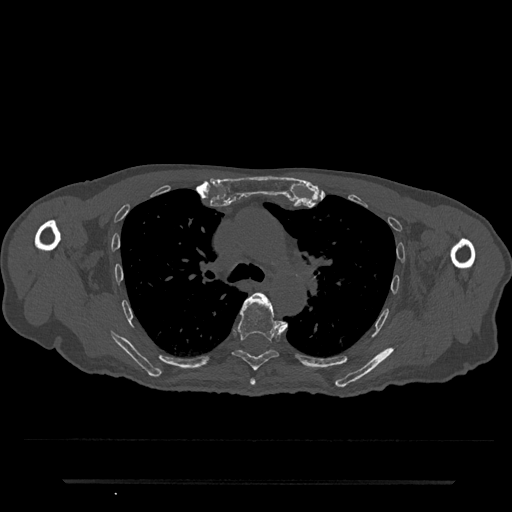
CT including the spine, one axial slice. Slice 534 of 797 in the series (ordered by position). Reconstruction kernel Br40s/3. 120 kVp. Bone window (W 1800 / L 400 HU). 0.5 mm slice thickness. 512 × 512 image matrix, field of view 427 × 427 mm. Male patient, age 74 years. Case-level facts recorded for this patient, not image findings: primary cancer: prostate.
Structures marked on this image (semi-automatically segmented with operator editing):
- T5 vertebra: box from (x=250, y=299) to (x=287, y=386) px
- T6 vertebra: (x=232, y=292)–(x=281, y=371)